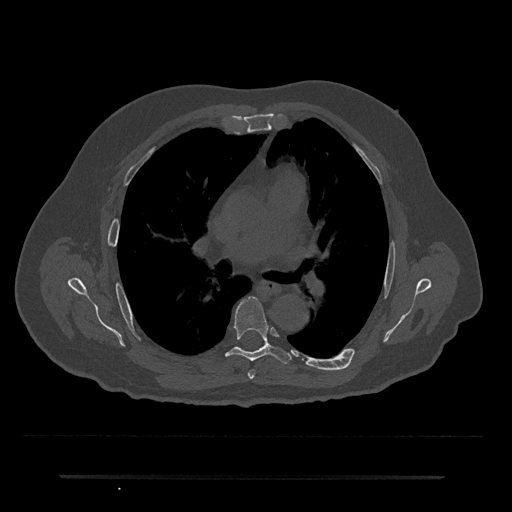
CT including the spine, one axial slice; position 439 of 797 along the scan axis; bone window (W 1800 / L 400 HU); 512 × 512 image matrix, field of view 437 × 437 mm. Male patient, age 69 years. From the clinical record (not read from this slice): primary cancer: prostate.
Structures marked on this image (semi-automatically segmented with operator editing):
- T5 vertebra: bounding box <248,370,255,379> (left, top, right, bottom; pixels)
- T6 vertebra: <226,297,291,364>